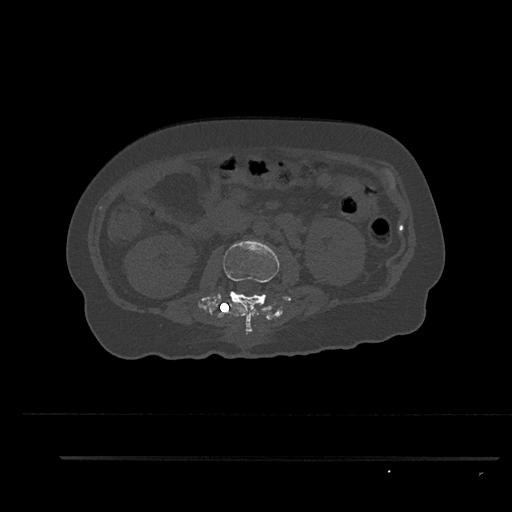
CT including the spine, one axial slice; position 142 of 797 along the scan axis; reconstruction kernel Br40s/3; 120 kVp; bone window (W 1800 / L 400 HU); 0.5 mm slice thickness; 512 × 512 image matrix. Patient: female, 44 years. Case-level facts recorded for this patient, not image findings: primary cancer: renal; vertebrae with lytic lesions (as recorded): L1.
Annotated regions visible in this slice (semi-automatically segmented with operator editing):
- L2 vertebra: bounding box <198,240,280,335> (left, top, right, bottom; pixels)